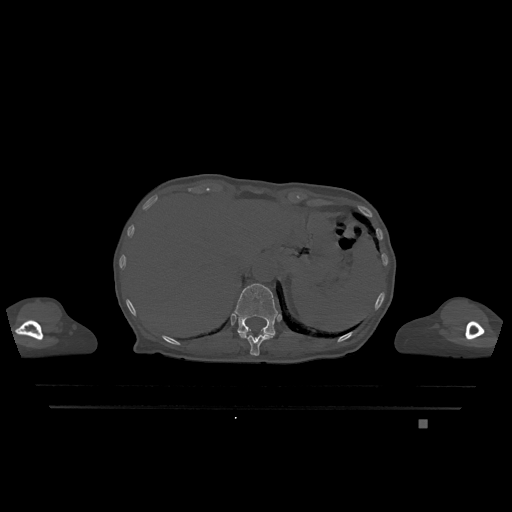
CT including the spine, one axial slice. Slice 555 of 1317 in the series (ordered by position). Bone window (W 1800 / L 400 HU). 0.5 mm slice thickness. 512 × 512 image matrix, field of view 500 × 500 mm. Patient: female, 74 years. Case-level facts recorded for this patient, not image findings: primary cancer: lung; vertebrae with lytic lesions (as recorded): T1, T4, T5, T6, L4, L5.
Outlined on this slice (semi-automatic segmentation, software-assisted and operator-edited):
- T11 vertebra: bounding box [x1, y1, x2, y2] px = [239, 333, 274, 356]
- T12 vertebra: [234, 283, 278, 336]